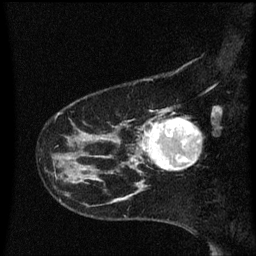
Breast MRI (dynamic contrast-enhanced), one sagittal slice; slice 14 of 60 in the series (ordered by position); dynamic contrast-enhanced series, image 2 of 3 at this slice position (ordered by acquisition); 1.5 T; TE 4.2 ms, TR 8.4 ms; 256 × 256 image matrix, field of view 200 × 200 mm. Patient: female, 41 years. Case-level facts recorded for this patient, not image findings: setting: breast cancer imaged before/during neoadjuvant chemotherapy; receptor status: triple-negative.
Annotated regions visible in this slice (semi-automatic segmentation, software-assisted and operator-edited):
- analysis volume of interest (the breast-tissue region the enhancement analysis was run in; not a lesion): box from (x=138, y=112) to (x=200, y=173) px
- tumour enhancement mask (voxels above the 70 % enhancement threshold inside the analysis volume of interest): (x=142, y=118)–(x=199, y=171)